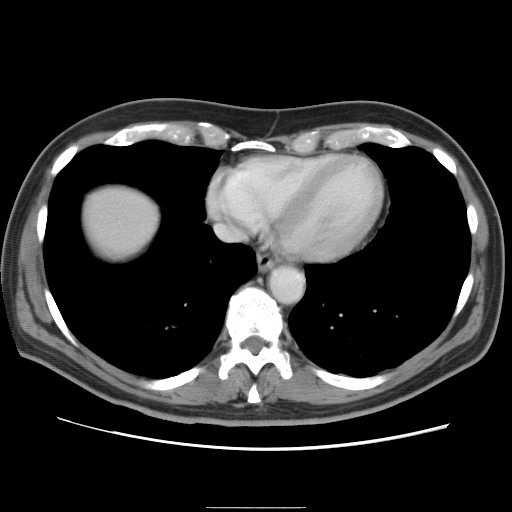
Contrast-enhanced abdominal CT, one axial slice; position 81 of 87 along the scan axis; intravenous contrast given; soft-tissue window (W 400 / L 40 HU); 5 mm slice thickness; 512 × 512 image matrix, field of view 363 × 363 mm. Male patient, age 63 years. Case-level facts recorded for this patient, not image findings: diagnosis: colorectal cancer liver metastases, imaged before liver resection; multiple liver metastases: no; largest metastasis: 9 cm; disease in both lobes: no.
Outlined on this slice (outlined manually by an expert reader):
- liver: bounding box (x1, y1, x2, y2) in pixels: (86, 187, 157, 254)
- planned liver remnant (the part of the liver to remain after resection): (87, 191, 158, 253)